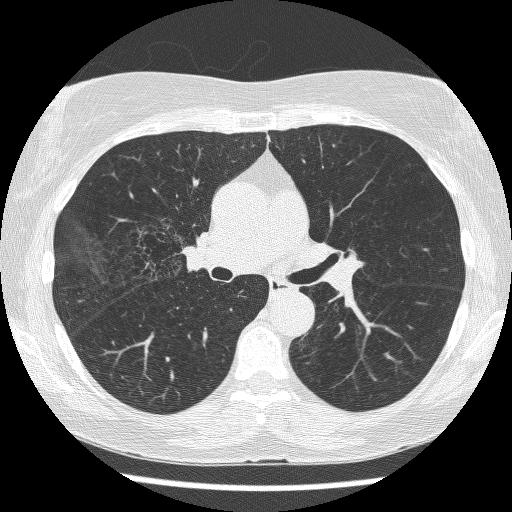
Low-dose screening chest CT, axial slice. First (baseline) screen. Lung window (W 1500 / L -600 HU). 1.25 mm slice thickness. Lung (sharp) reconstruction kernel (BONE). 512 × 512 image matrix, field of view 316 × 316 mm. Female, age 64 years at enrolment. Former smoker at enrolment.
Expert reader's lesion annotation, bounding box [x1, y1, x2, y2] px = [122, 215, 198, 276]. The screening reader recorded 3 non-calcified nodules or masses ≥4 mm on this exam (right upper lobe, right upper lobe, left lower lobe); which of them this box marks is not recorded. Participant outcome: lung cancer diagnosed 735 days after this screen — adenocarcinoma, NOS, right upper lobe, right middle lobe, right hilum, stage IV (AJCC 6th edition), 85 mm at pathology.